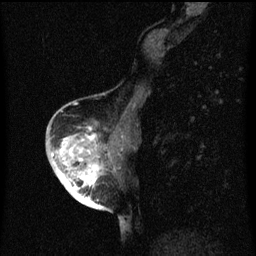
Breast MRI (dynamic contrast-enhanced), one sagittal slice; slice 26 of 60 in the series (ordered by position); dynamic contrast-enhanced series, image 2 of 3 at this slice position (ordered by acquisition); 1.5 T; TE 4.2 ms, TR 8 ms; 256 × 256 image matrix, field of view 180 × 180 mm. Patient: female, 56 years.
Outlined on this slice (semi-automatic segmentation, software-assisted and operator-edited):
- analysis volume of interest (the breast-tissue region the enhancement analysis was run in; not a lesion): box from (x=54, y=128) to (x=120, y=199) px
- tumour enhancement mask (voxels above the 70 % enhancement threshold inside the analysis volume of interest): (x=55, y=128)–(x=101, y=199)